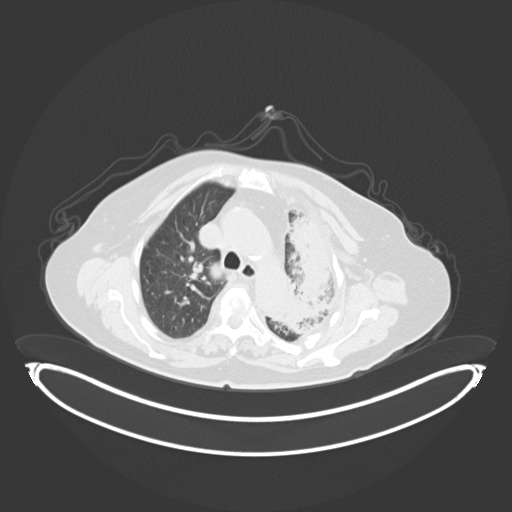
Chest CT, one axial slice; position 217 of 284 along the scan axis; reconstruction kernel B30f; 120 kVp; lung window (W 1500 / L -600 HU); 3 mm slice thickness; 512 × 512 image matrix, field of view 500 × 500 mm. Patient: female, 75 years. From the clinical record (not read from this slice): clinical TNM (as recorded): T3 N3 M1.
Annotated regions visible in this slice (rectangle marked by the reading radiologist):
- lung tumour (recorded histology: adenocarcinoma): box from (x=270, y=208) to (x=336, y=338) px